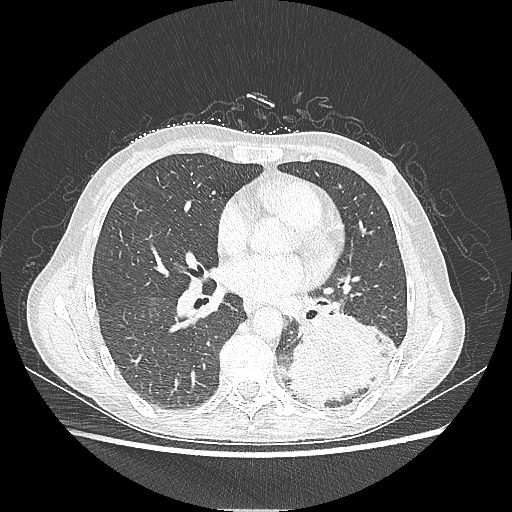
Chest CT, one axial slice; position 107 of 220 along the scan axis; reconstruction kernel LUNG; lung window (W 1500 / L -600 HU); 1.25 mm slice thickness; 512 × 512 image matrix, field of view 360 × 360 mm. Patient: female, 53 years. From the clinical record (not read from this slice): clinical TNM (as recorded): T3 N0 M0.
Structures marked on this image (bounding box drawn by a radiologist):
- lung tumour (recorded histology: adenocarcinoma): bounding box <287,307,398,411> (left, top, right, bottom; pixels)